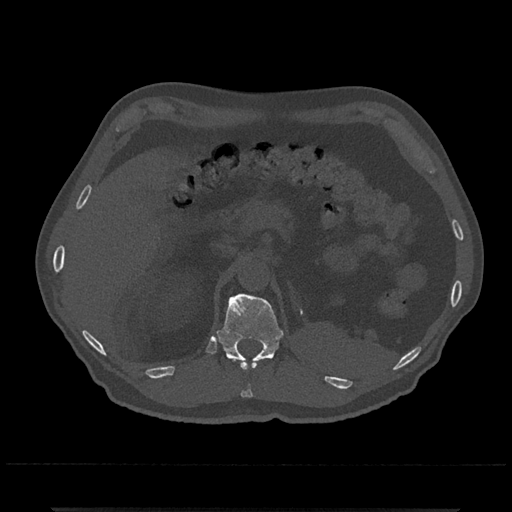
CT including the spine, one axial slice; position 446 of 797 along the scan axis; reconstruction kernel Br40s/3; 120 kVp; bone window (W 1800 / L 400 HU); 512 × 512 image matrix, field of view 393 × 393 mm. Patient: male, 67 years. Case-level facts recorded for this patient, not image findings: primary cancer: prostate.
Outlined on this slice (semi-automatically segmented with operator editing):
- T11 vertebra: bounding box <229,358,257,398> (left, top, right, bottom; pixels)
- T12 vertebra: <216,293,284,367>